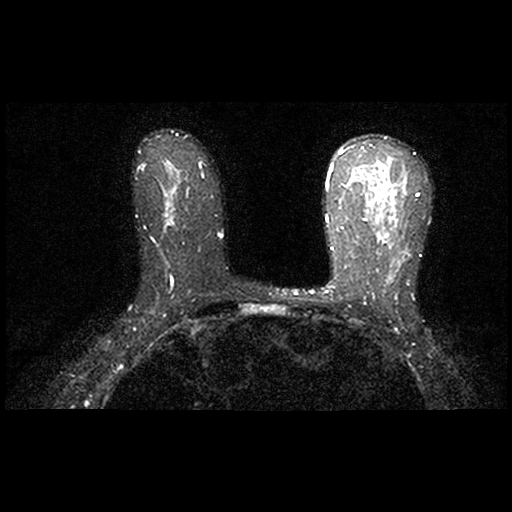
Breast MRI examination; 2 images, each one mid-volume slice chosen by position. Patient in her 40s.
Image 1: axial T2-weighted / STIR image, series "STIR SENSE", slice 43 of 84, 2 mm slice thickness.
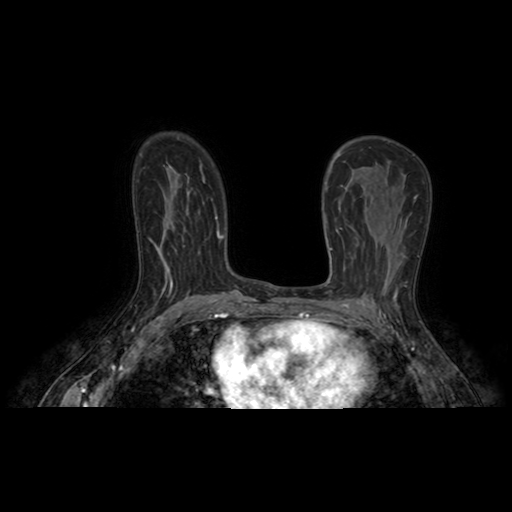
Image 2: axial dynamic contrast-enhanced T1-weighted image, slice 43 of 84, dynamic phase 6 of 10, 4 mm slice thickness.
Patient-level pathology facts (from the clinical record, not from the images): pathology diagnosis: invasive intraductal (left breast); clinical background (as recorded): history of left breast cancer (invasive ductal cancer), status post left partial mastectomy.